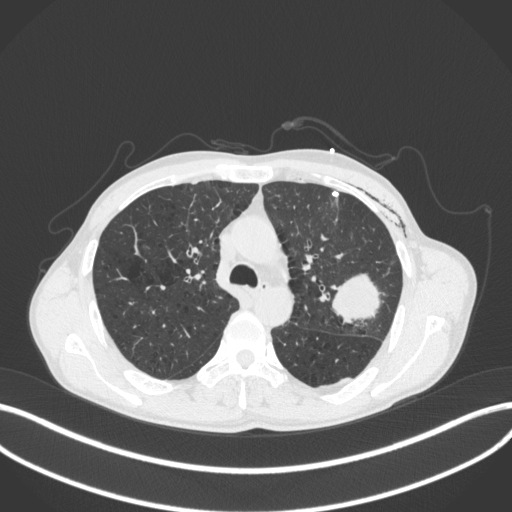
Chest CT, one axial slice. Position 274 of 416 along the scan axis. 120 kVp. Lung window (W 1500 / L -600 HU). 1 mm slice thickness. 512 × 512 image matrix, field of view 400 × 400 mm. Male patient, age 58 years. Case-level facts recorded for this patient, not image findings: clinical TNM (as recorded): T3 N0 M0.
Structures marked on this image (bounding box drawn by a radiologist):
- lung tumour (recorded histology: adenocarcinoma): box from (x=326, y=260) to (x=384, y=323) px